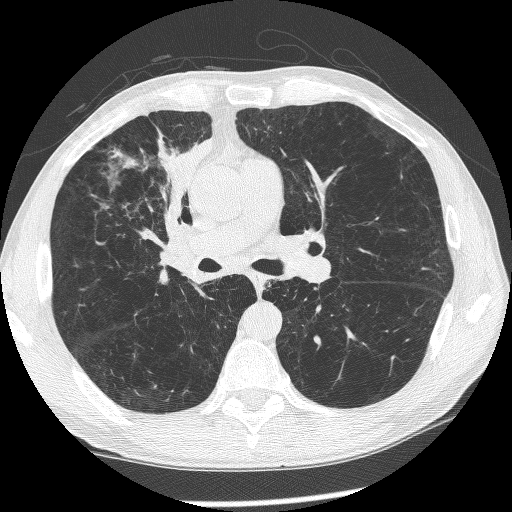
Chest CT (low-dose screening protocol), one axial image, baseline annual screen, lung window (W 1500 / L -600 HU), 1.25 mm slice thickness, slice 141 of 266 in the series. Male participant, aged 60 years at enrolment. Current smoker at enrolment.
Lesion marked by an expert reader, box from (x=145, y=184) to (x=218, y=278) px. Screening reader's record for this exam (one nodule recorded; not confirmed to be the boxed lesion): non-calcified nodule or mass ≥4 mm, right upper lobe, 12 × 8 mm, spiculated (stellate) margins, mixed attenuation. Participant outcome: lung cancer diagnosed 208 days after this screen — squamous cell carcinoma, NOS, right upper lobe, right middle lobe, right main stem bronchus, poorly differentiated (G3), stage IV (AJCC 6th edition).